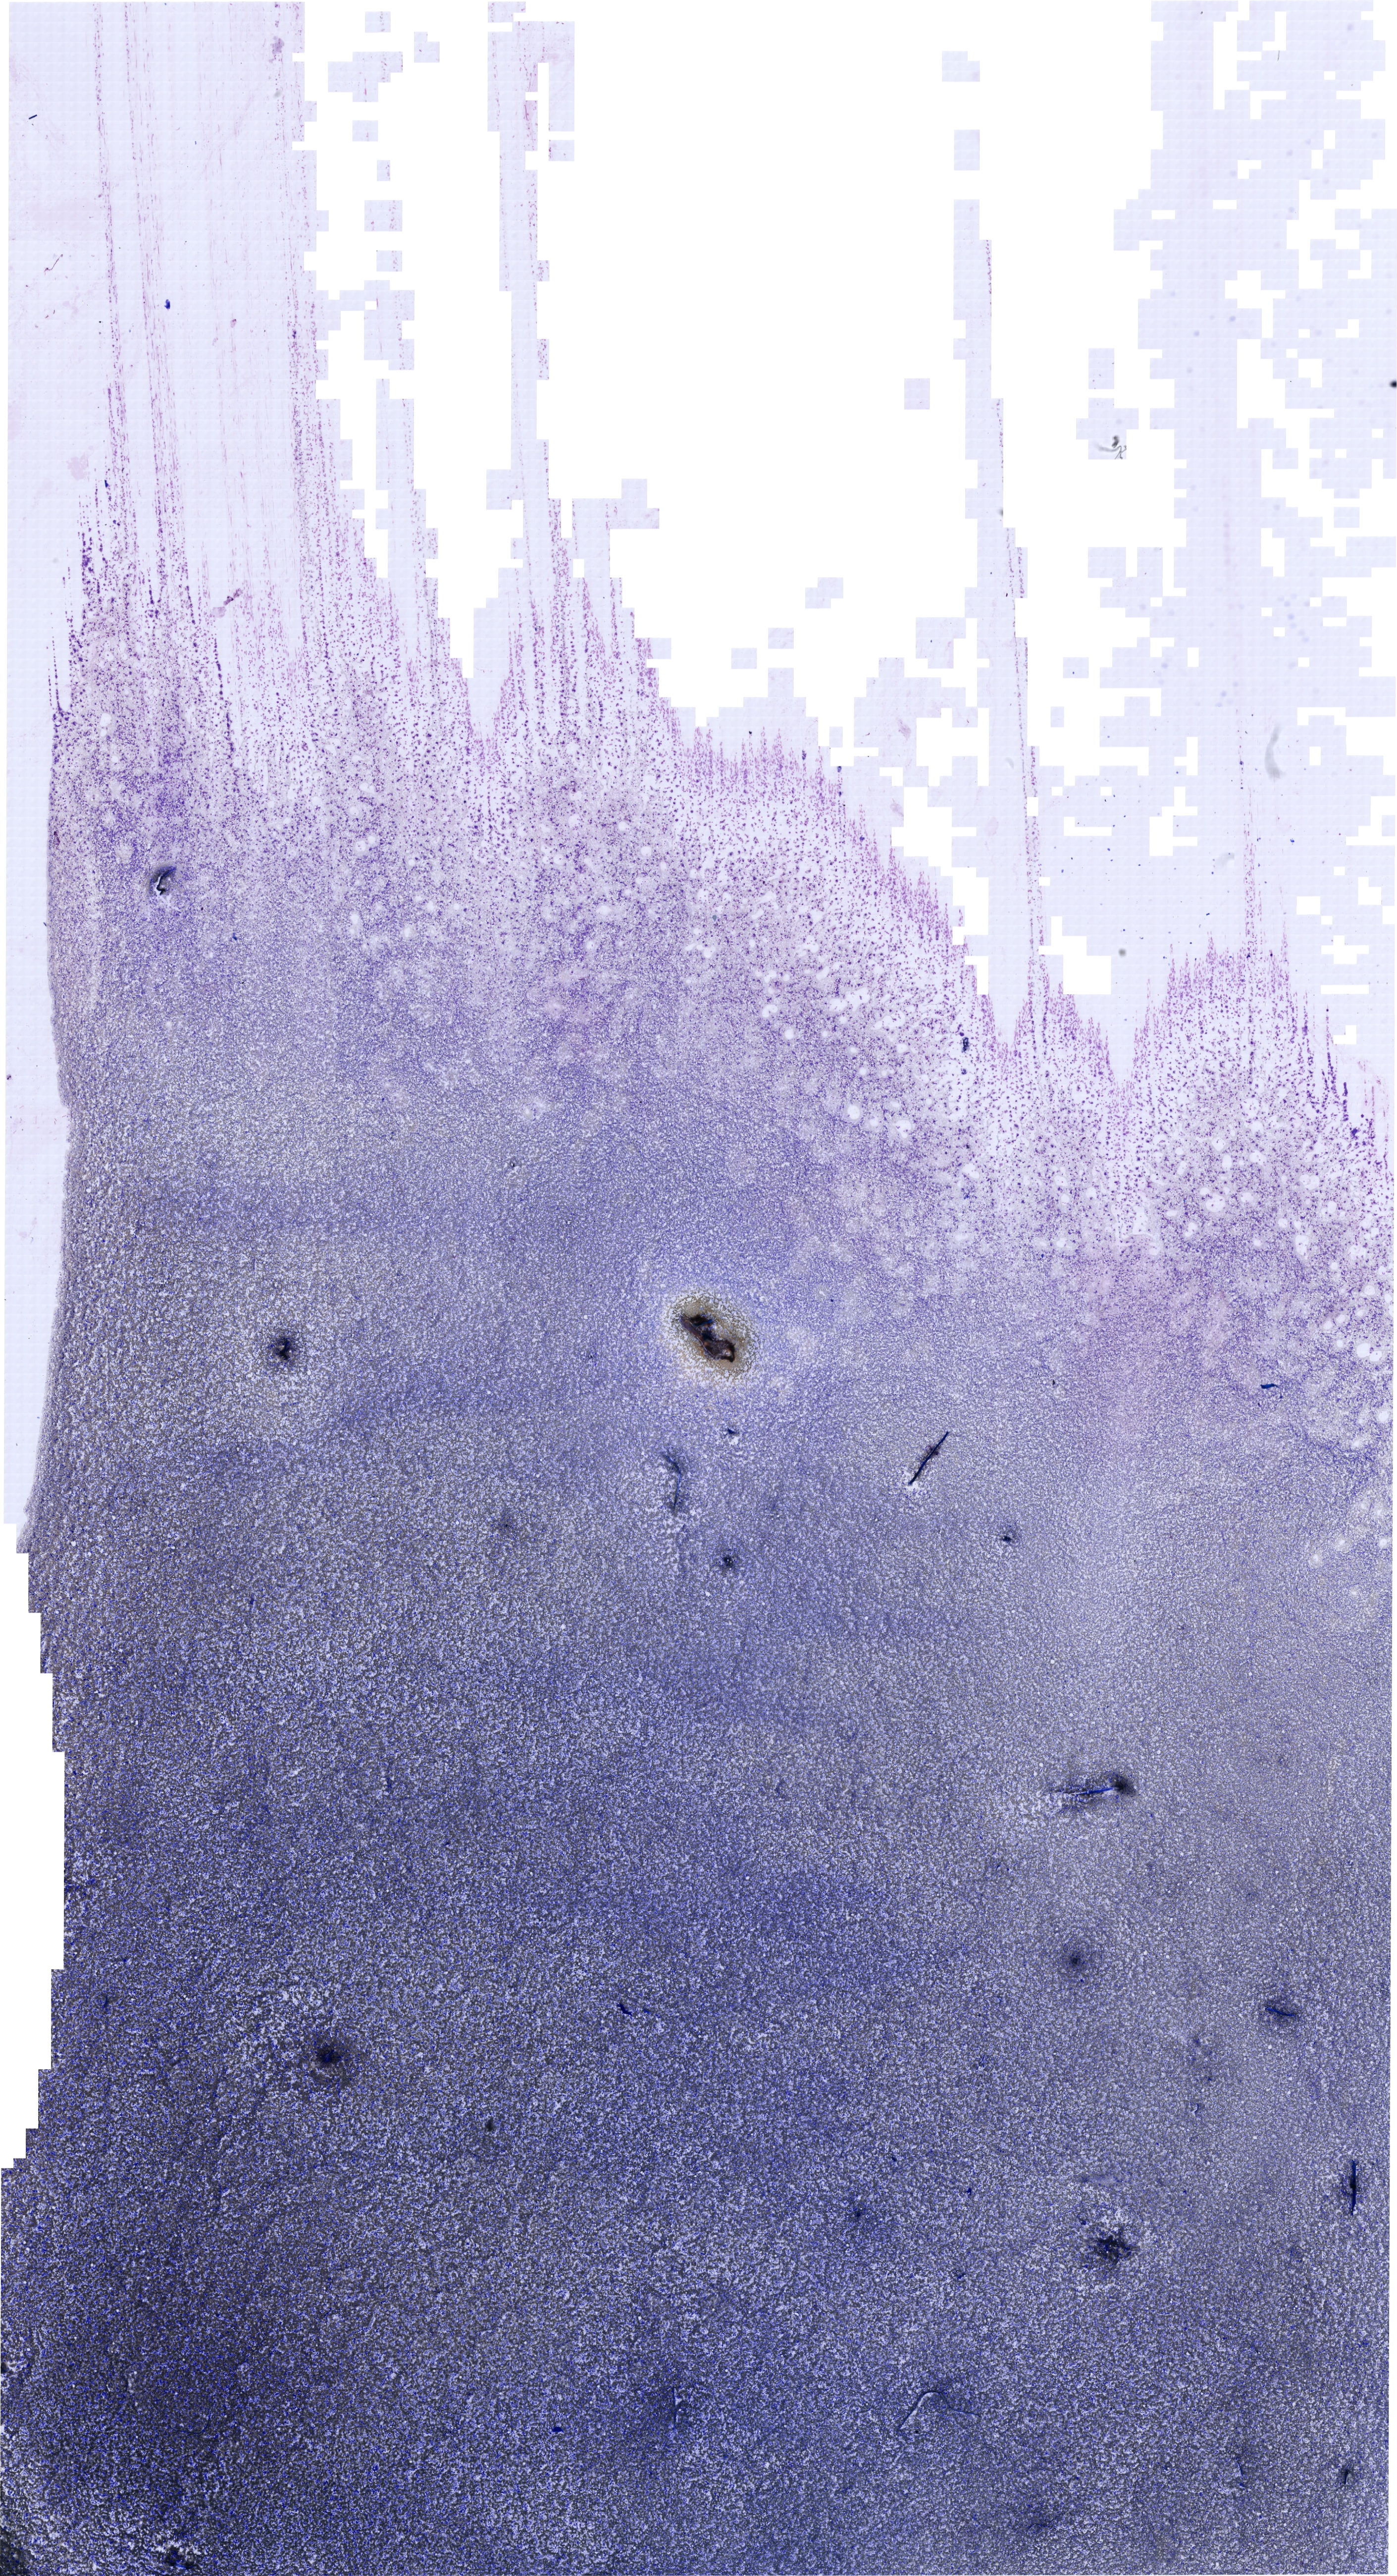
Whole-slide image of a May-Grünwald–Giemsa-stained bone marrow aspirate smear, low-resolution overview of the scanned area, about 22.0 x 40.6 mm. Male patient.
Diagnosis: Burkitt Leukemia.